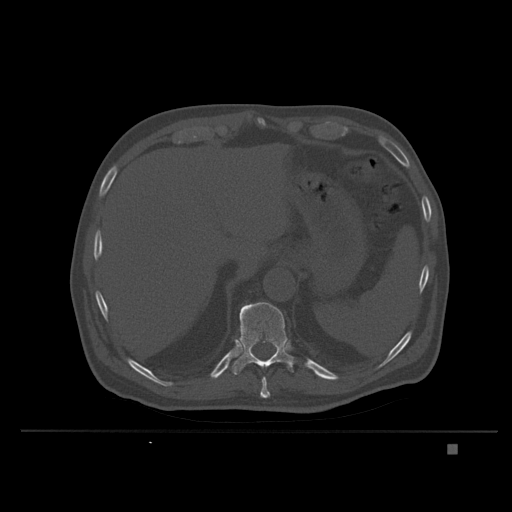
CT including the spine, one axial slice; position 180 of 435 along the scan axis; bone window (W 1800 / L 400 HU); 1.5 mm slice thickness; 512 × 512 image matrix, field of view 434 × 434 mm. Patient: male, 73 years. From the clinical record (not read from this slice): primary cancer: skin.
Outlined on this slice (semi-automatic segmentation, software-assisted and operator-edited):
- T10 vertebra: box from (x=260, y=377) to (x=270, y=398) px
- T11 vertebra: (x=232, y=302)–(x=295, y=375)